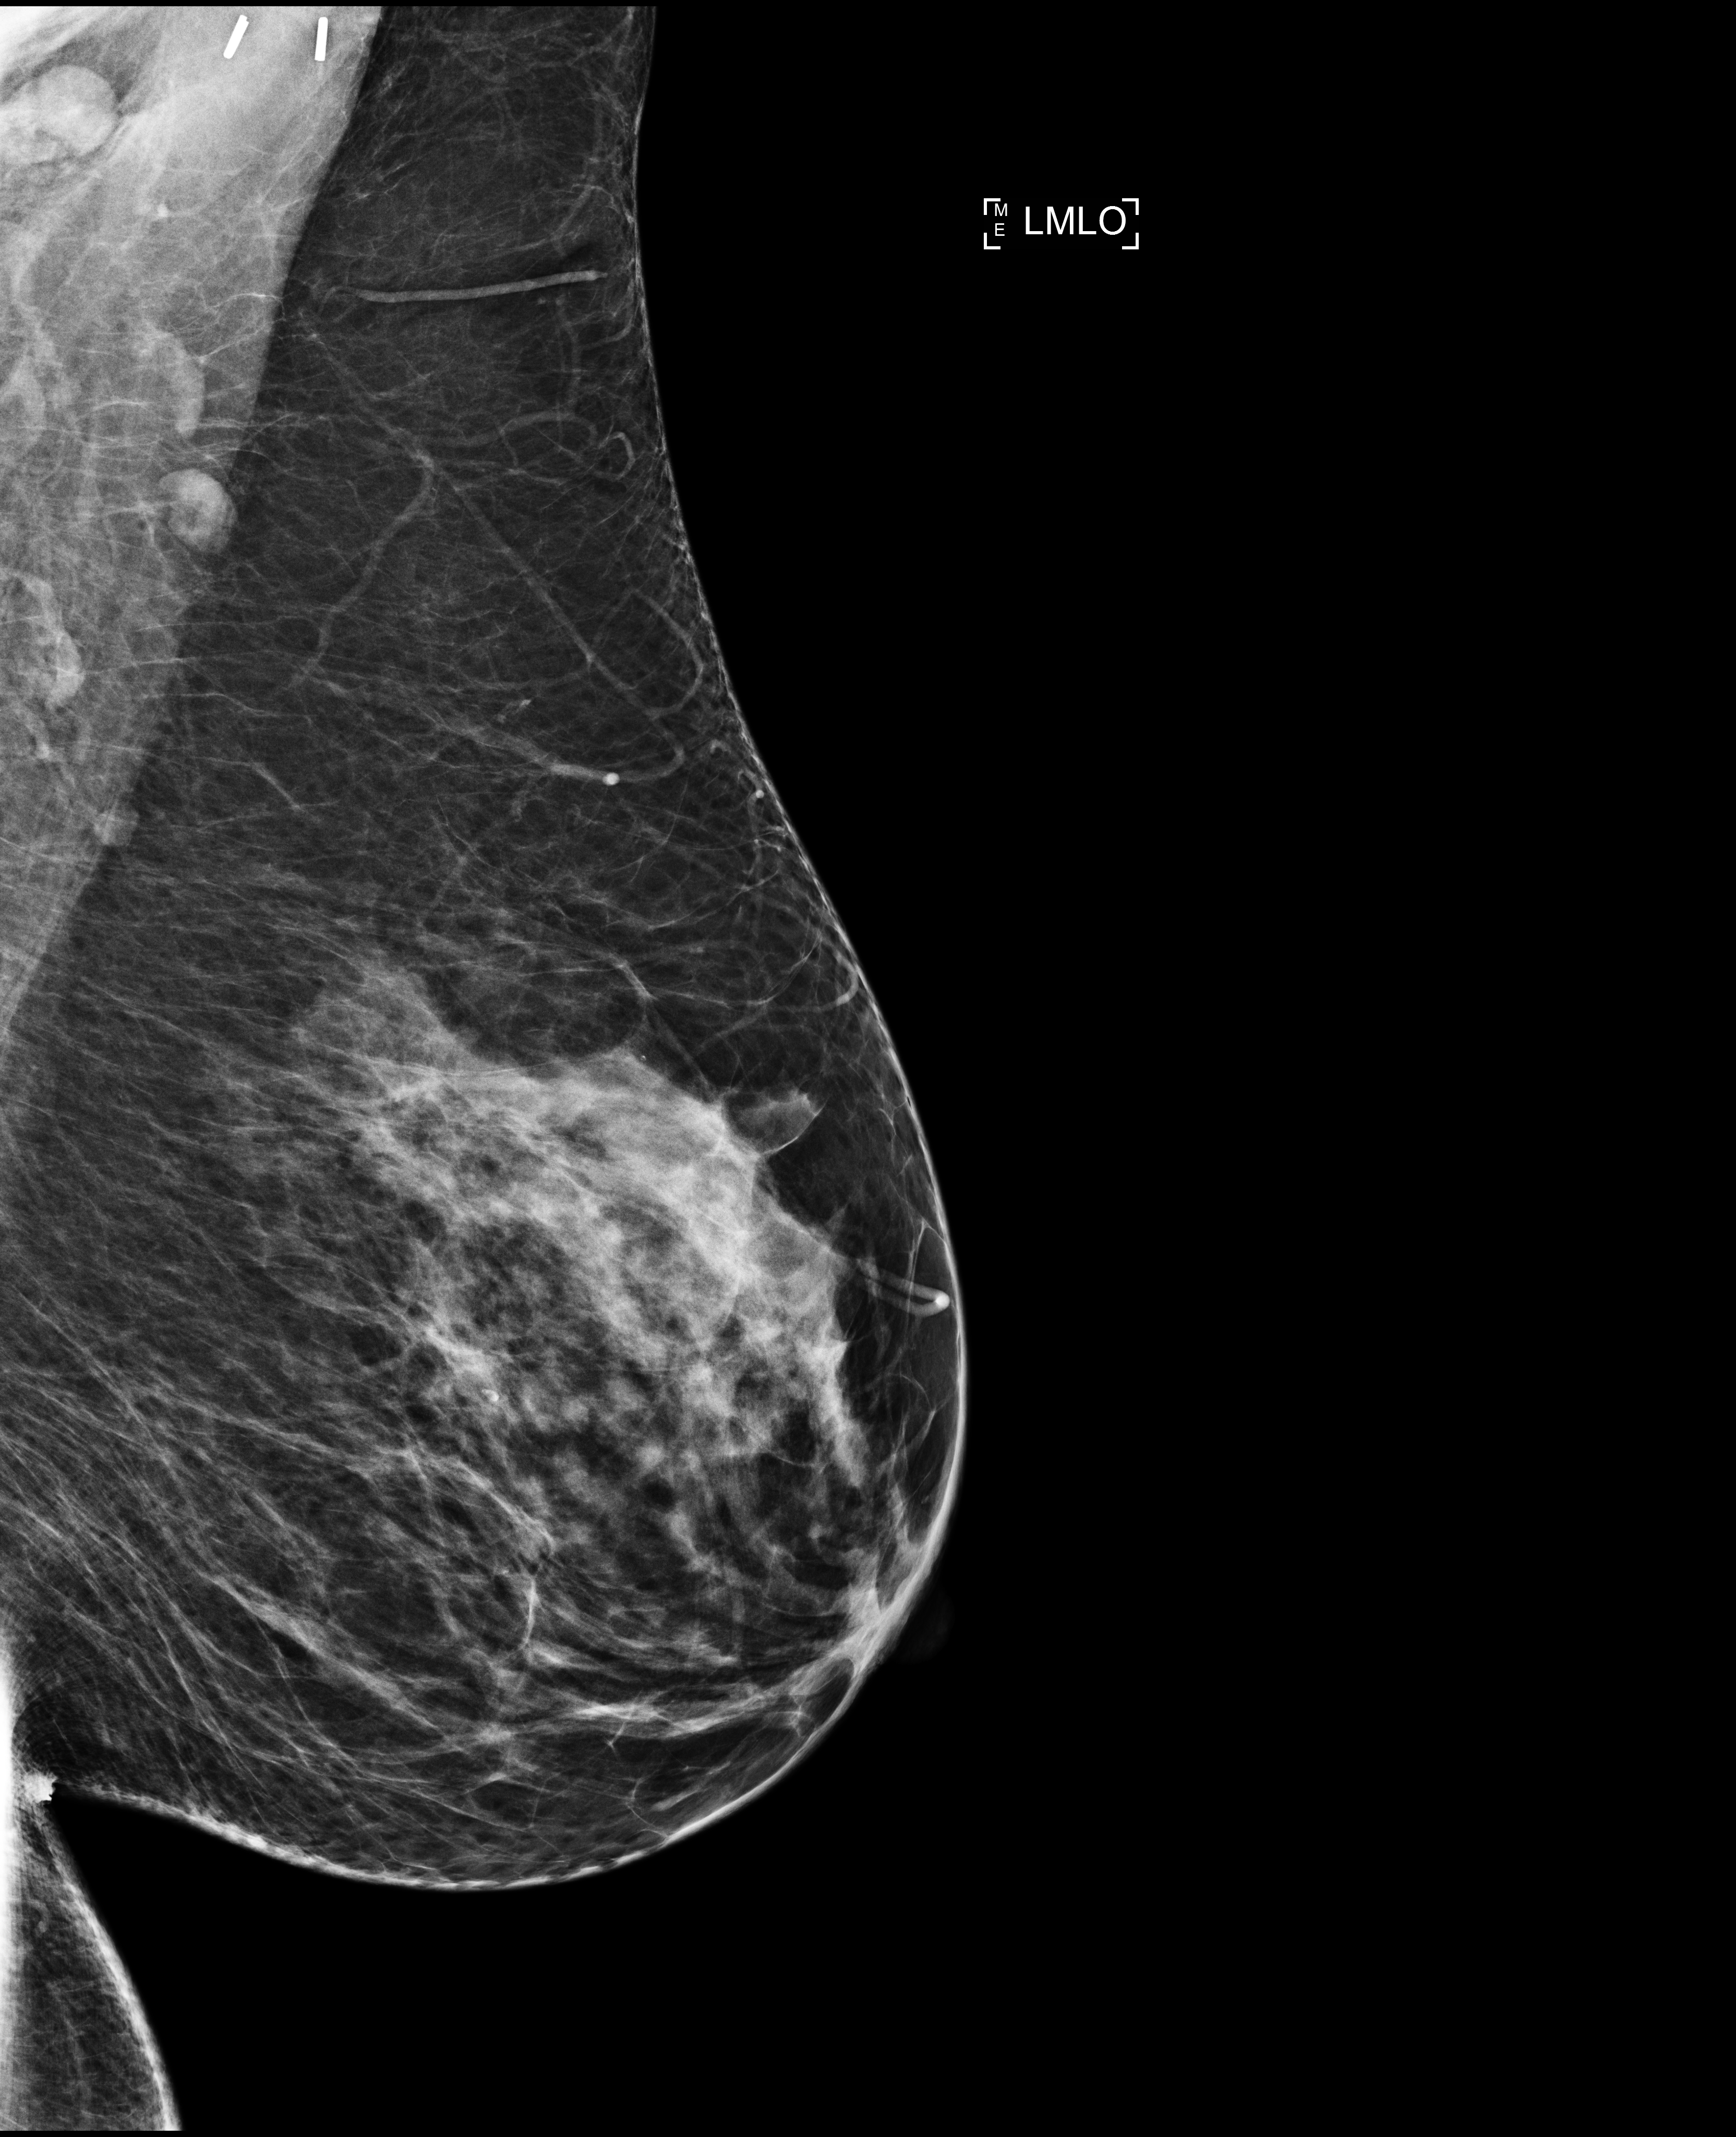
Annual screening mammography examination, compressed breast thickness 68 mm. Female patient, age 52 years.
Image type: full-field digital mammogram. Breast: left. Projection: medio-lateral oblique projection.